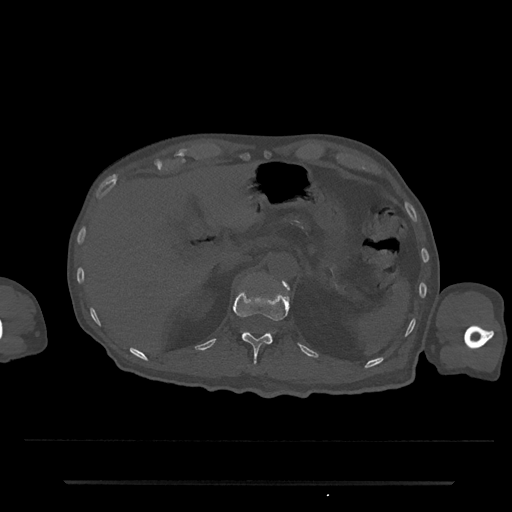
CT including the spine, one axial slice; slice 183 of 797 in the series (ordered by position); reconstruction kernel Br40s/3; 120 kVp; bone window (W 1800 / L 400 HU); 0.5 mm slice thickness; 512 × 512 image matrix. Patient: male, 74 years. From the clinical record (not read from this slice): primary cancer: prostate.
Annotated regions visible in this slice (semi-automatic segmentation, software-assisted and operator-edited):
- L1 vertebra: bounding box (x1, y1, x2, y2) in pixels: (243, 282, 289, 333)
- T12 vertebra: (234, 290, 289, 361)